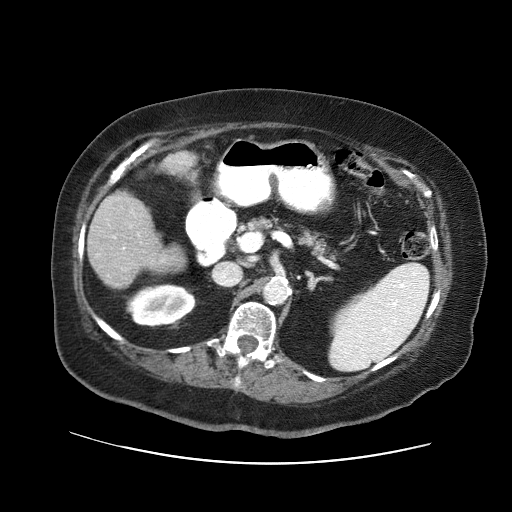
Contrast-enhanced abdominal CT (liver protocol), one axial slice; slice 18 of 71 in the series (ordered by position); reconstruction kernel STANDARD; soft-tissue window (W 400 / L 40 HU); 2.5 mm slice thickness; 512 × 512 image matrix, field of view 400 × 400 mm. Case-level facts recorded for this patient, not image findings: diagnosis: hepatocellular carcinoma (patient treated with transarterial chemoembolisation; whether this scan precedes or follows treatment is not stated here); TNM stage (as recorded): Stage-II; Child-Pugh class: A; tumour differentiation: poorly differentiated; tumour nodularity: multinodular.
Annotated regions visible in this slice (semi-automatic segmentation, software-assisted and operator-edited):
- liver parenchyma outside the tumour (the mass and vessels are separate outlines, so this box may not span the whole liver): bounding box (x1, y1, x2, y2) in pixels: (88, 152, 196, 288)
- liver vessels: (114, 236, 116, 238)